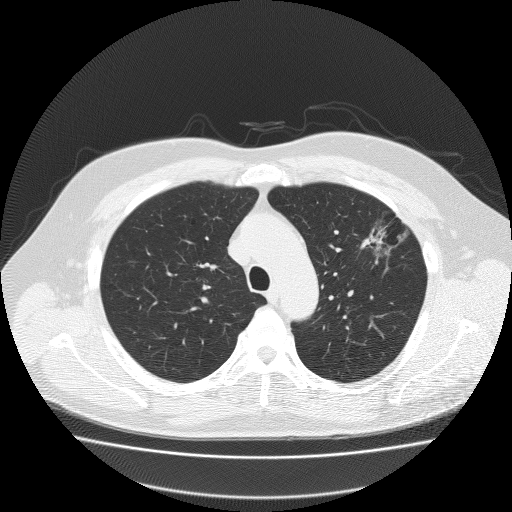
Low-dose screening chest CT, axial slice. Baseline screening round. Lung window (W 1500 / L -600 HU). 2 mm slice thickness. Lung (sharp) reconstruction kernel (FC51). 512 × 512 image matrix. Male, age 62 years at enrolment.
Lesion marked by an expert reader, bounding box [x1, y1, x2, y2] px = [353, 205, 421, 263]. The exam's reader record, not a measurement of the box and not confirmed to be the same lesion: non-calcified nodule or mass ≥4 mm, left upper lobe, 18 × 8 mm, spiculated (stellate) margins, soft tissue attenuation.